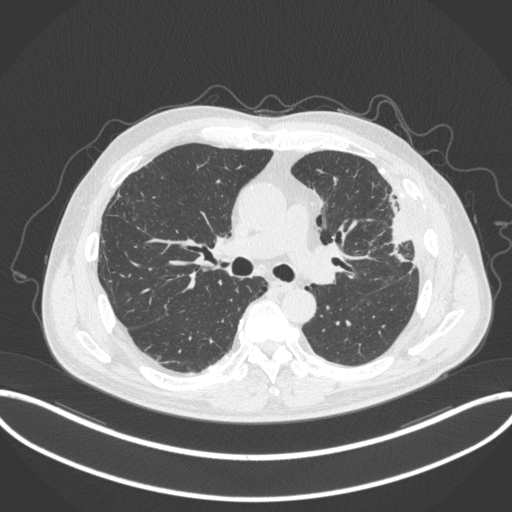
Chest CT, one axial slice; position 205 of 382 along the scan axis; 120 kVp; lung window (W 1500 / L -600 HU); 1 mm slice thickness; 512 × 512 image matrix, field of view 415 × 415 mm. Male patient, age 64 years. From the clinical record (not read from this slice): clinical TNM (as recorded): T4 N1 M0.
Annotated regions visible in this slice (bounding box drawn by a radiologist):
- lung tumour (recorded histology: adenocarcinoma): bounding box [x1, y1, x2, y2] px = [376, 185, 415, 264]